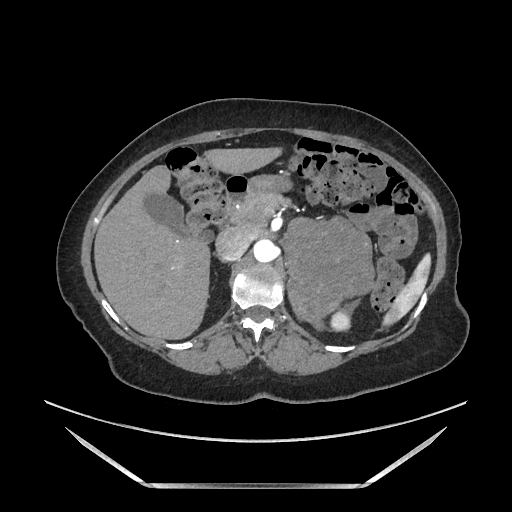
Contrast-enhanced abdominal CT, one axial slice; slice 106 of 205 in the series (ordered by position); soft-tissue window (W 400 / L 40 HU); 1.25 mm slice thickness; 512 × 512 image matrix, field of view 440 × 440 mm. Female patient. Case-level facts recorded for this patient, not image findings: diagnosis: adrenocortical carcinoma; tumour side: left adrenal; tumour size at pathology: 12.5 cm; Ki-67 index: 39 %; stage (as recorded): 3.
Outlined on this slice (semi-automatic segmentation, software-assisted and operator-edited):
- mass: bounding box <286,221,372,326> (left, top, right, bottom; pixels)